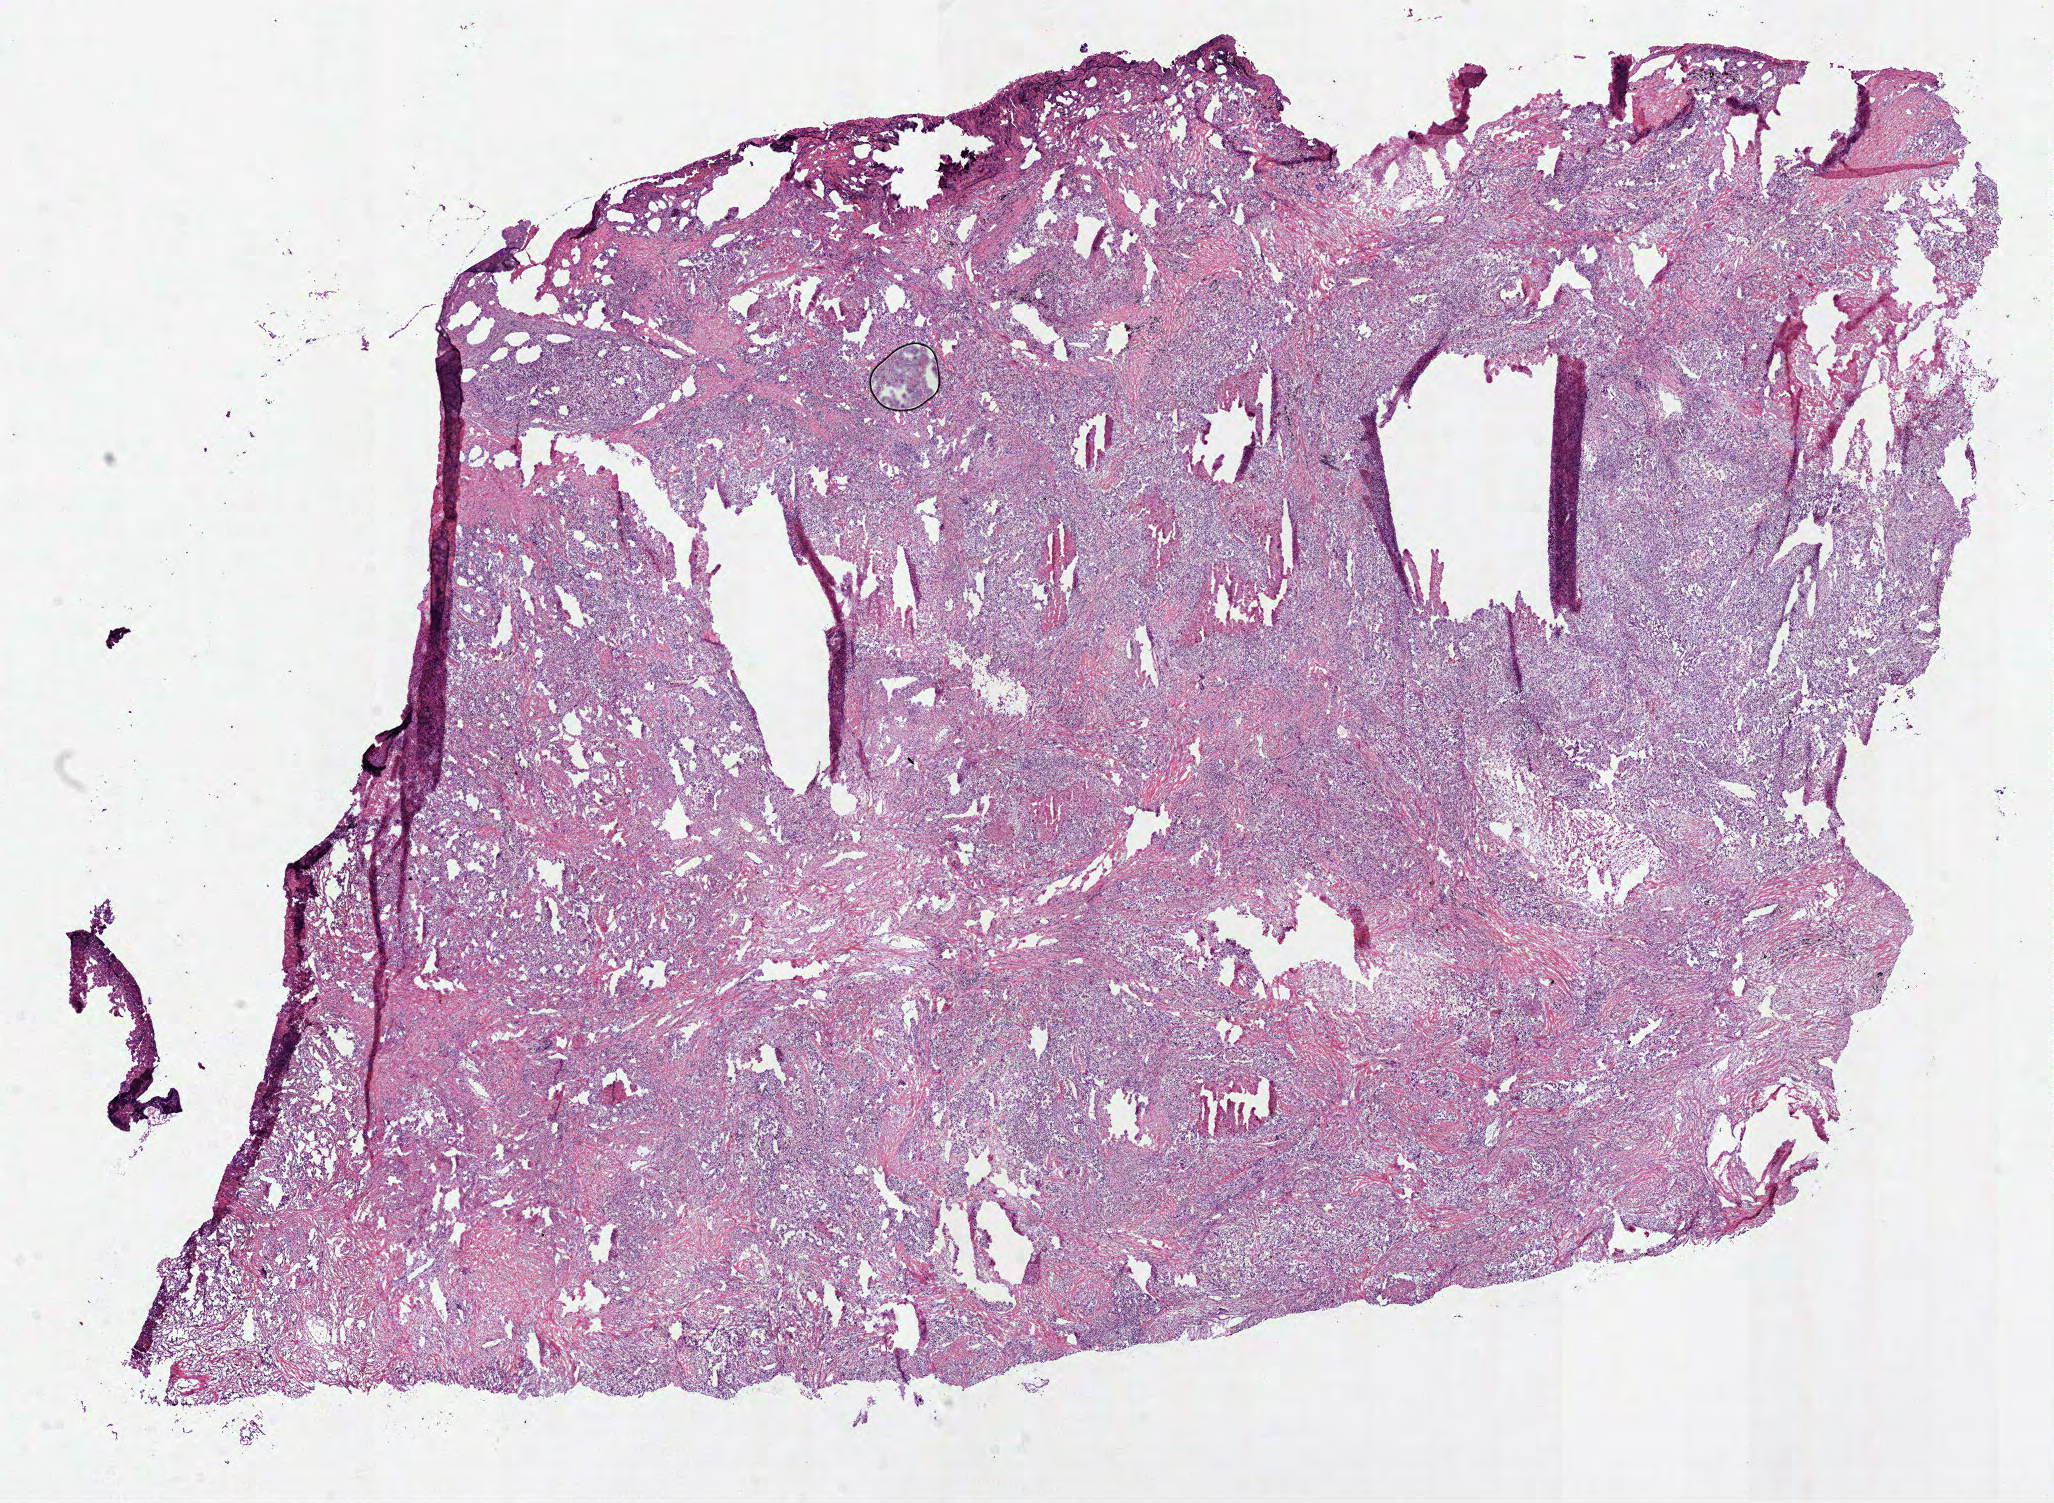
Digitized Hematoxylin and eosin (H&E) stained tissue section (whole slide), whole scanned area (about 16.6 x 12.1 mm) shown as a low-resolution overview. Frozen section from the top of the tissue portion. Lung, primary tumour sample. Male, age 72 years at initial diagnosis. Composition of this section per pathologist review: tumour cells 80%, tumour nuclei 70%, normal cells 0%, stromal cells 5%, necrosis 15%. Inflammatory infiltration, as recorded: lymphocyte infiltration 10%, monocyte infiltration 2%, neutrophil infiltration 5%.
TNM: T4 N2 M0. AJCC pathologic stage: IIIB (5th edition). Histologic diagnosis: Adenocarcinoma, NOS (lower lobe, lung). Laterality: left.